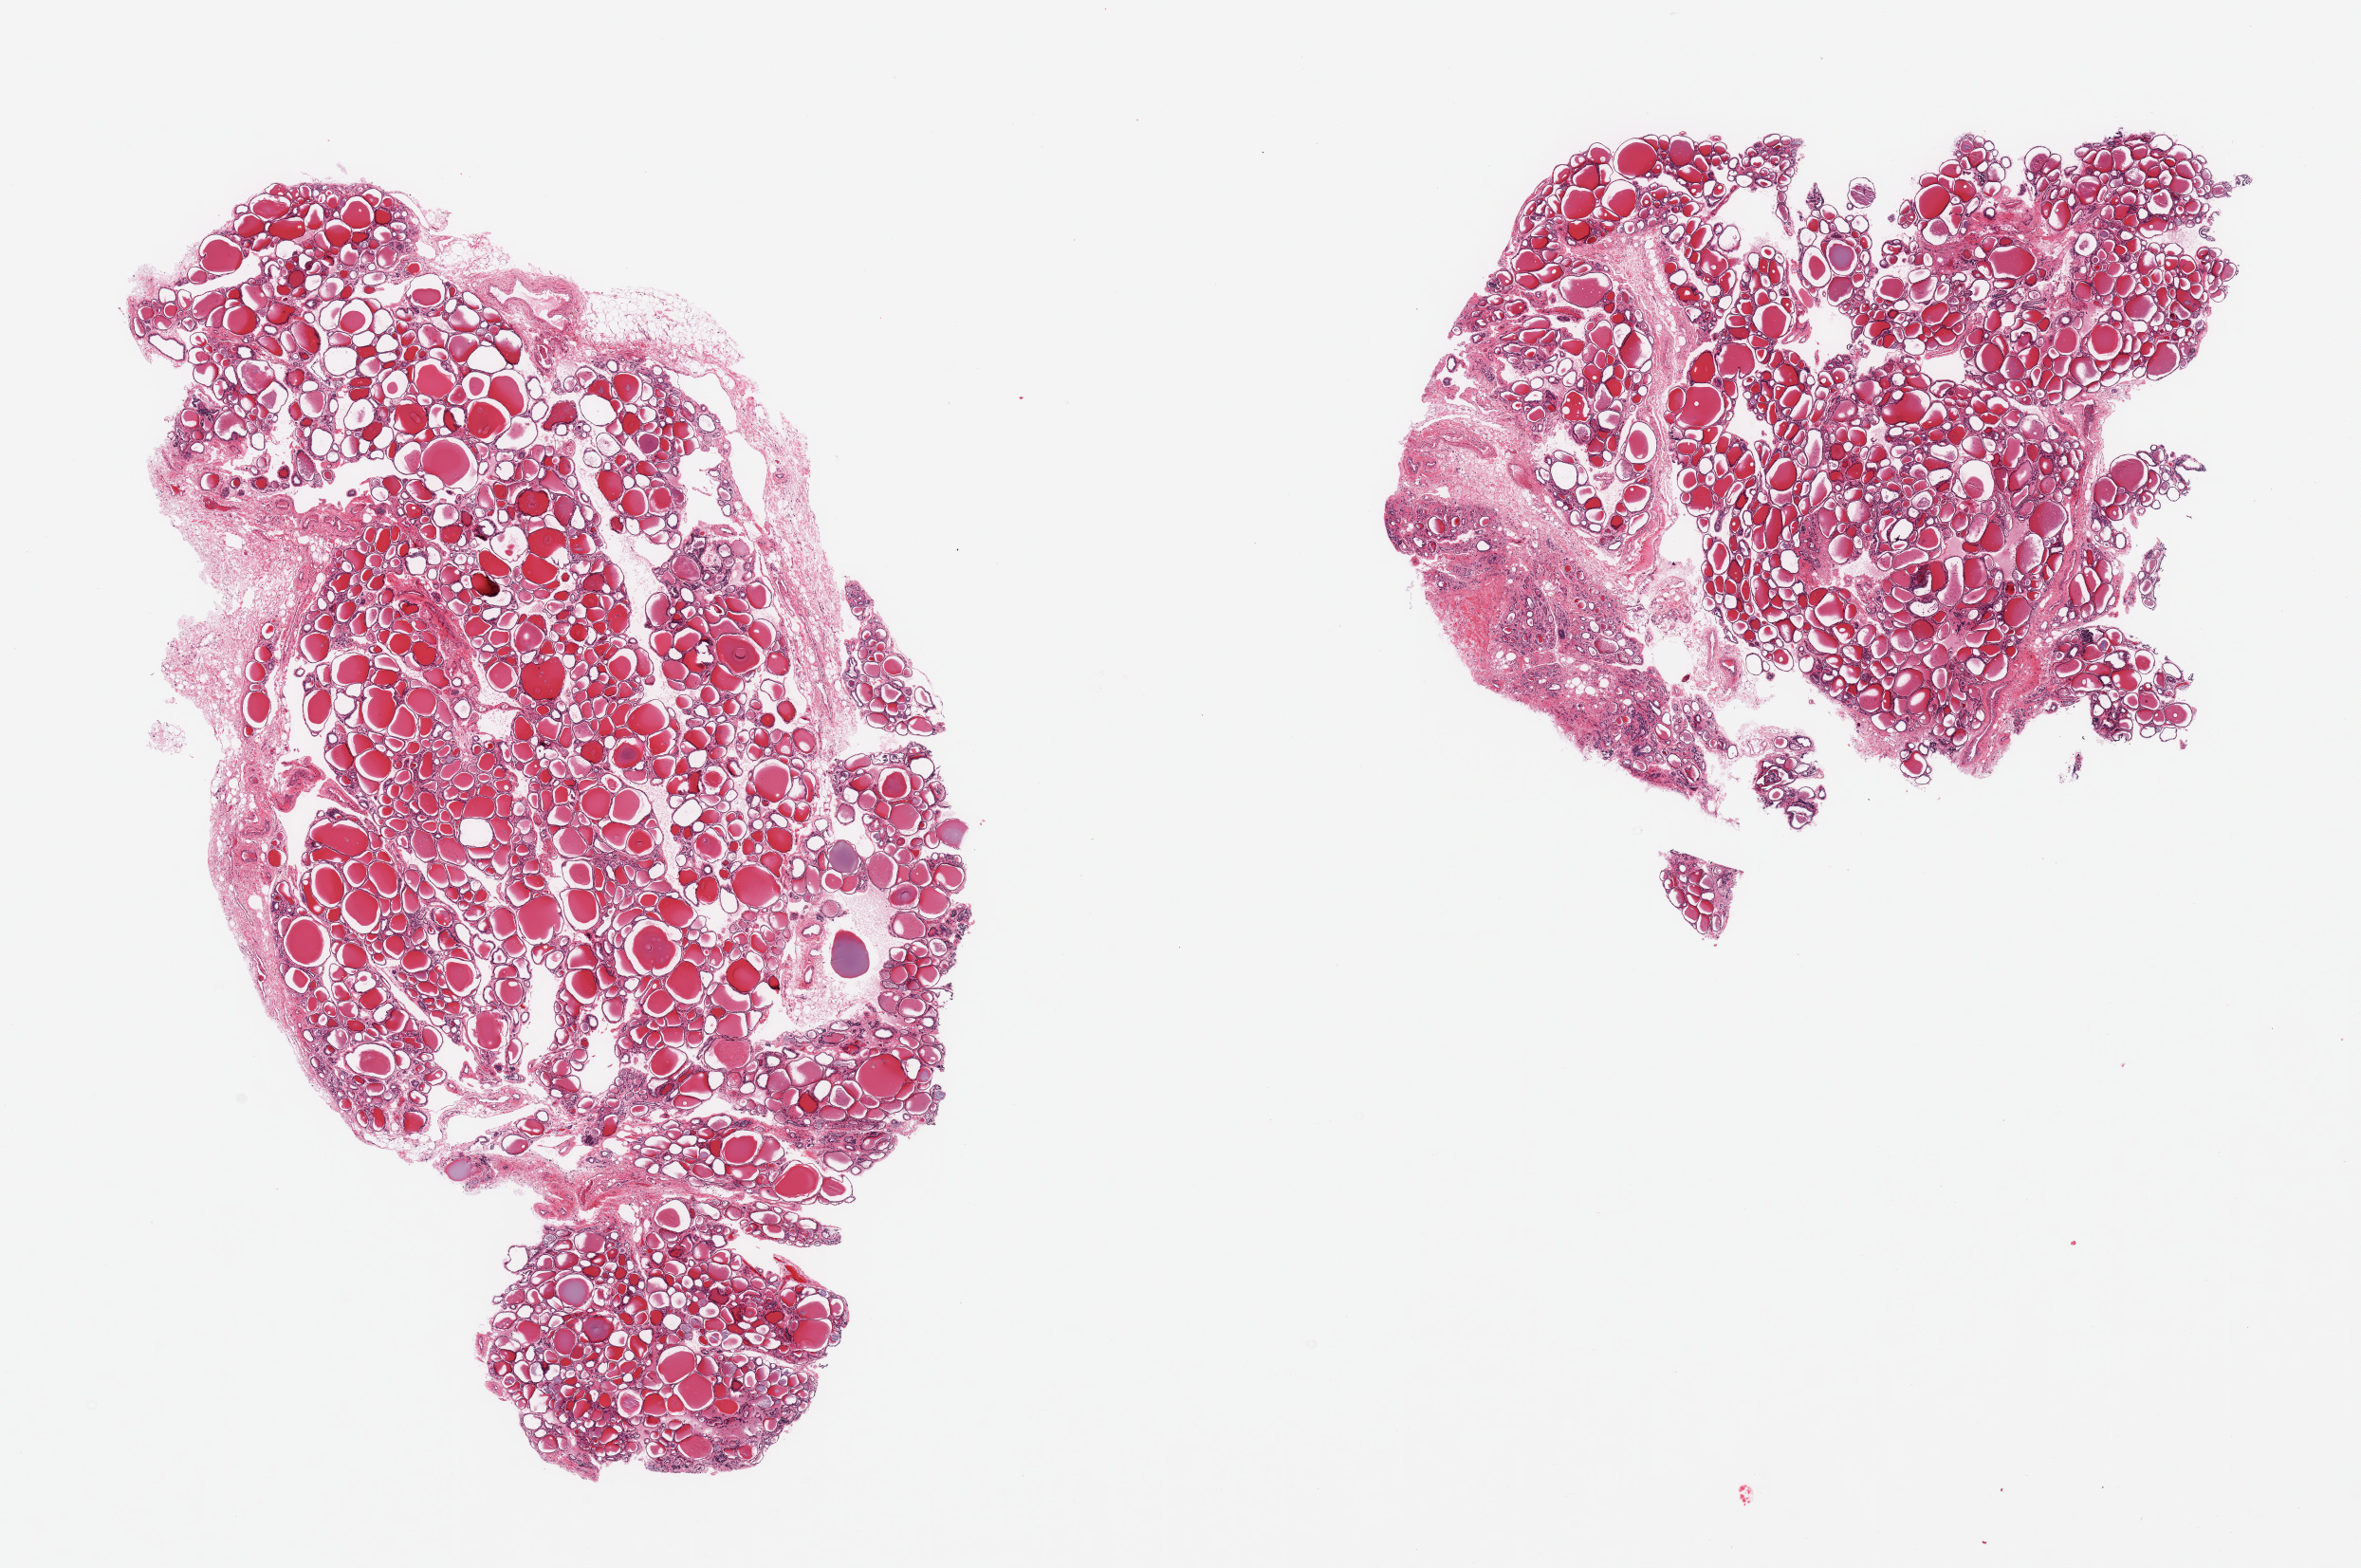
H&E whole-slide image — whole scanned area (about 19.7 x 13.1 mm, slide scanned at 20x) shown as a low-resolution overview, PAXgene-fixed, paraffin-embedded tissue, section of thyroid (target tissue), tissue donor sample.
- reviewer comment on this tissue sample: 2 pieces, regressive changes